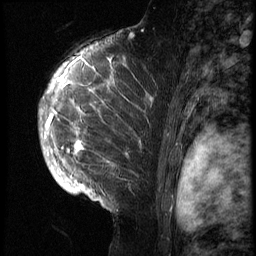
Breast MRI (dynamic contrast-enhanced), one sagittal slice. Slice 46 of 70 in the series (ordered by position). 3 images stored at this slice position (order not interpretable as contrast timing). 1.5 T. TE 4.2 ms, TR 9 ms. 2.5 mm slice thickness. 256 × 256 image matrix, field of view 180 × 180 mm. Female patient, age 28 years. From the clinical record (not read from this slice): setting: breast cancer imaged before/during neoadjuvant chemotherapy.
Outlined on this slice (semi-automatic segmentation, software-assisted and operator-edited):
- analysis volume of interest (the breast-tissue region the enhancement analysis was run in; not a lesion): bounding box <43,42,158,215> (left, top, right, bottom; pixels)
- tumour enhancement mask (voxels above the 140 % enhancement threshold inside the analysis volume of interest): <45,47,113,201>